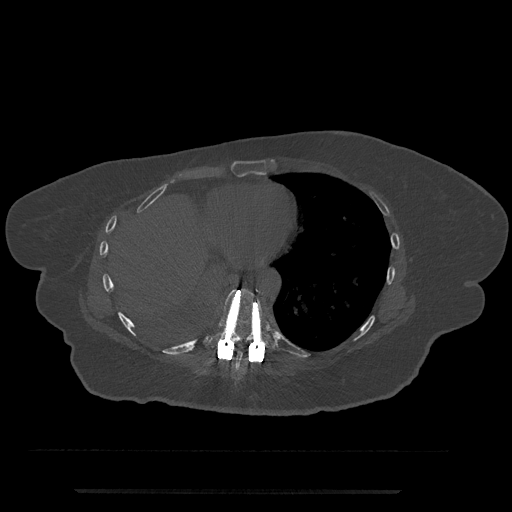
CT including the spine, one axial slice. Bone window (W 1800 / L 400 HU). 0.5 mm slice thickness. 512 × 512 image matrix, field of view 440 × 440 mm. Female patient, age 51 years. From the clinical record (not read from this slice): primary cancer: neuro; vertebrae with lytic lesions (as recorded): T8.
Outlined on this slice (semi-automatically segmented with operator editing):
- T8 vertebra: bounding box (x1, y1, x2, y2) in pixels: (196, 345, 250, 373)
- T9 vertebra: (204, 288, 276, 353)